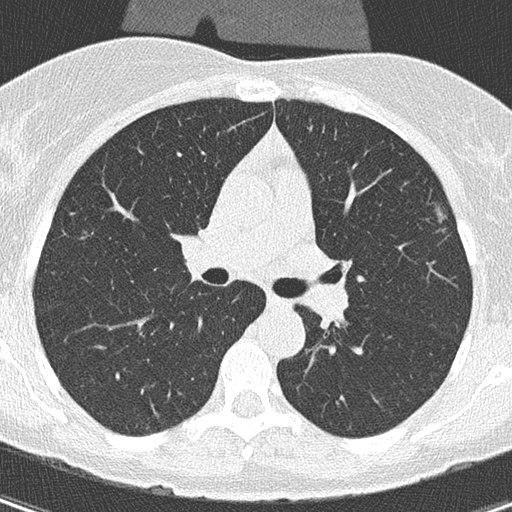
Axial slice from a low-dose chest CT screening exam. First (baseline) screen. Lung window (W 1500 / L -600 HU). 2 mm slice thickness. 512 × 512 image matrix, field of view 270 × 270 mm. Female, age 56 years at enrolment. Former smoker at enrolment.
Expert-annotated lung lesion, bounding box (x1, y1, x2, y2) in pixels: (419, 194, 464, 251). Screening reader's record for this exam (one nodule recorded; not confirmed to be the boxed lesion): non-calcified nodule or mass ≥4 mm, left upper lobe, 110 × 106 mm, spiculated (stellate) margins, soft tissue attenuation. Lung cancer was diagnosed 417 days after this screen: adenocarcinoma, NOS, left upper lobe, moderately differentiated (G2), stage IA (AJCC 6th edition), 11 mm at pathology.